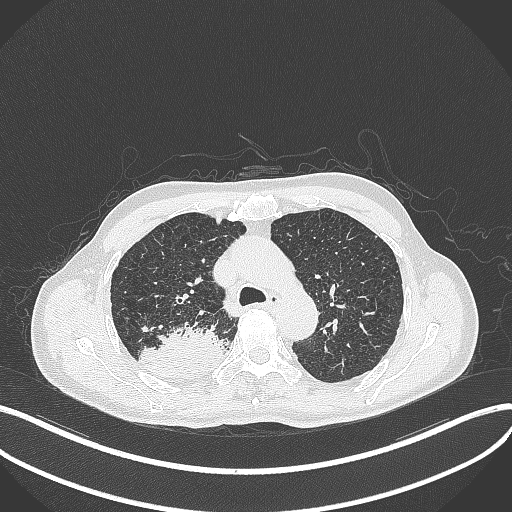
Chest CT, one axial slice. Position 323 of 428 along the scan axis. 120 kVp. Lung window (W 1500 / L -600 HU). 1 mm slice thickness. 512 × 512 image matrix, field of view 400 × 400 mm. Male patient, age 79 years. From the clinical record (not read from this slice): clinical TNM (as recorded): T3 N0 M0.
Outlined on this slice (rectangle marked by the reading radiologist):
- lung tumour (recorded histology: adenocarcinoma): bounding box <137,320,231,380> (left, top, right, bottom; pixels)